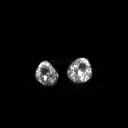
FDG PET of an extremity soft-tissue mass (from a PET/CT study), one axial slice; position 197 of 267 along the scan axis; 3.27 mm slice thickness; 128 × 128 image matrix, field of view 700 × 700 mm. Patient: male, 44 years. From the clinical record (not read from this slice): histological type: undifferentiated pleomorphic liposarcoma; grade: high; site of the primary tumour: left thigh.
Outlined on this slice (expert contour drawn on MRI and transferred to this co-registered scan by the dataset authors):
- gross tumour volume including surrounding oedema: bounding box [x1, y1, x2, y2] px = [71, 70, 86, 76]